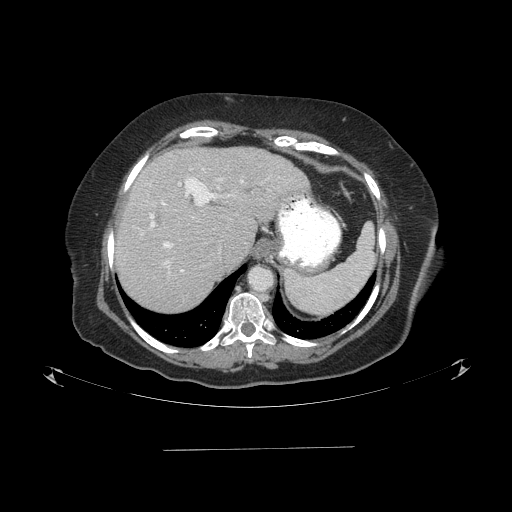
Contrast-enhanced abdominal CT (liver protocol), one axial slice; position 68 of 103 along the scan axis; reconstruction kernel STANDARD; one of 2 acquisitions stored at this slice position; soft-tissue window (W 400 / L 40 HU); 2.5 mm slice thickness; 512 × 512 image matrix, field of view 500 × 500 mm. From the clinical record (not read from this slice): diagnosis: hepatocellular carcinoma (patient treated with transarterial chemoembolisation; whether this scan precedes or follows treatment is not stated here); TNM stage (as recorded): Stage-IIIA; Child-Pugh class: A; tumour size: 5.2 cm.
Outlined on this slice (semi-automatically segmented with operator editing):
- liver parenchyma outside the tumour (the mass and vessels are separate outlines, so this box may not span the whole liver): bounding box (x1, y1, x2, y2) in pixels: (114, 146, 309, 312)
- liver vessels: (141, 169, 244, 272)